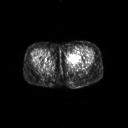
FDG PET of an extremity soft-tissue mass (from a PET/CT study), one axial slice; slice 16 of 267 in the series (ordered by position); 3.27 mm slice thickness; 128 × 128 image matrix. Female patient, age 47 years. Case-level facts recorded for this patient, not image findings: histological type: myxofibrosarcoma; grade: intermediate; site of the primary tumour: left thigh.
Annotated regions visible in this slice (expert contour drawn on MRI and transferred to this co-registered scan by the dataset authors):
- gross tumour volume including surrounding oedema: bounding box <67,53,81,63> (left, top, right, bottom; pixels)
- gross tumour volume (mass): <69,53,80,60>